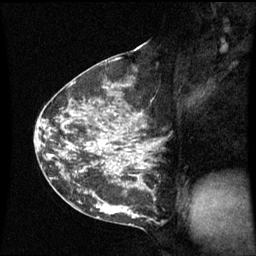
Breast MRI (dynamic contrast-enhanced), one sagittal slice; slice 30 of 60 in the series (ordered by position); dynamic contrast-enhanced series, image 2 of 3 at this slice position (ordered by acquisition); 1.5 T; TE 4.2 ms, TR 8.9 ms; 256 × 256 image matrix. Patient: female, 42 years. Case-level facts recorded for this patient, not image findings: setting: breast cancer imaged before/during neoadjuvant chemotherapy; receptor status: HER2-positive.
Outlined on this slice (semi-automatic segmentation, software-assisted and operator-edited):
- analysis volume of interest (the breast-tissue region the enhancement analysis was run in; not a lesion): box from (x=62, y=93) to (x=157, y=210) px
- tumour enhancement mask (voxels above the 70 % enhancement threshold inside the analysis volume of interest): (x=70, y=114)–(x=144, y=169)